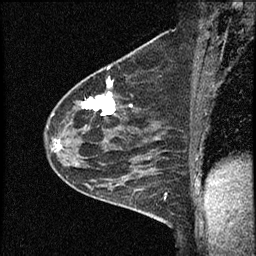
Breast MRI (dynamic contrast-enhanced), one sagittal slice; position 42 of 60 along the scan axis; dynamic contrast-enhanced study with each time point stored as its own series, time point 2 of 4 at this slice position (early post-contrast, ordered by acquisition time); 1.5 T; TE 4.2 ms, TR 17.6 ms; 256 × 256 image matrix, field of view 200 × 200 mm. Patient: female, 53 years. From the clinical record (not read from this slice): setting: breast cancer imaged before/during neoadjuvant chemotherapy; receptor status: HR-positive, HER2-negative.
Annotated regions visible in this slice (semi-automatically segmented with operator editing):
- analysis volume of interest (the breast-tissue region the enhancement analysis was run in; not a lesion): bounding box [x1, y1, x2, y2] px = [44, 69, 156, 199]
- tumour enhancement mask (voxels above the 100 % enhancement threshold inside the analysis volume of interest): [54, 79, 115, 149]